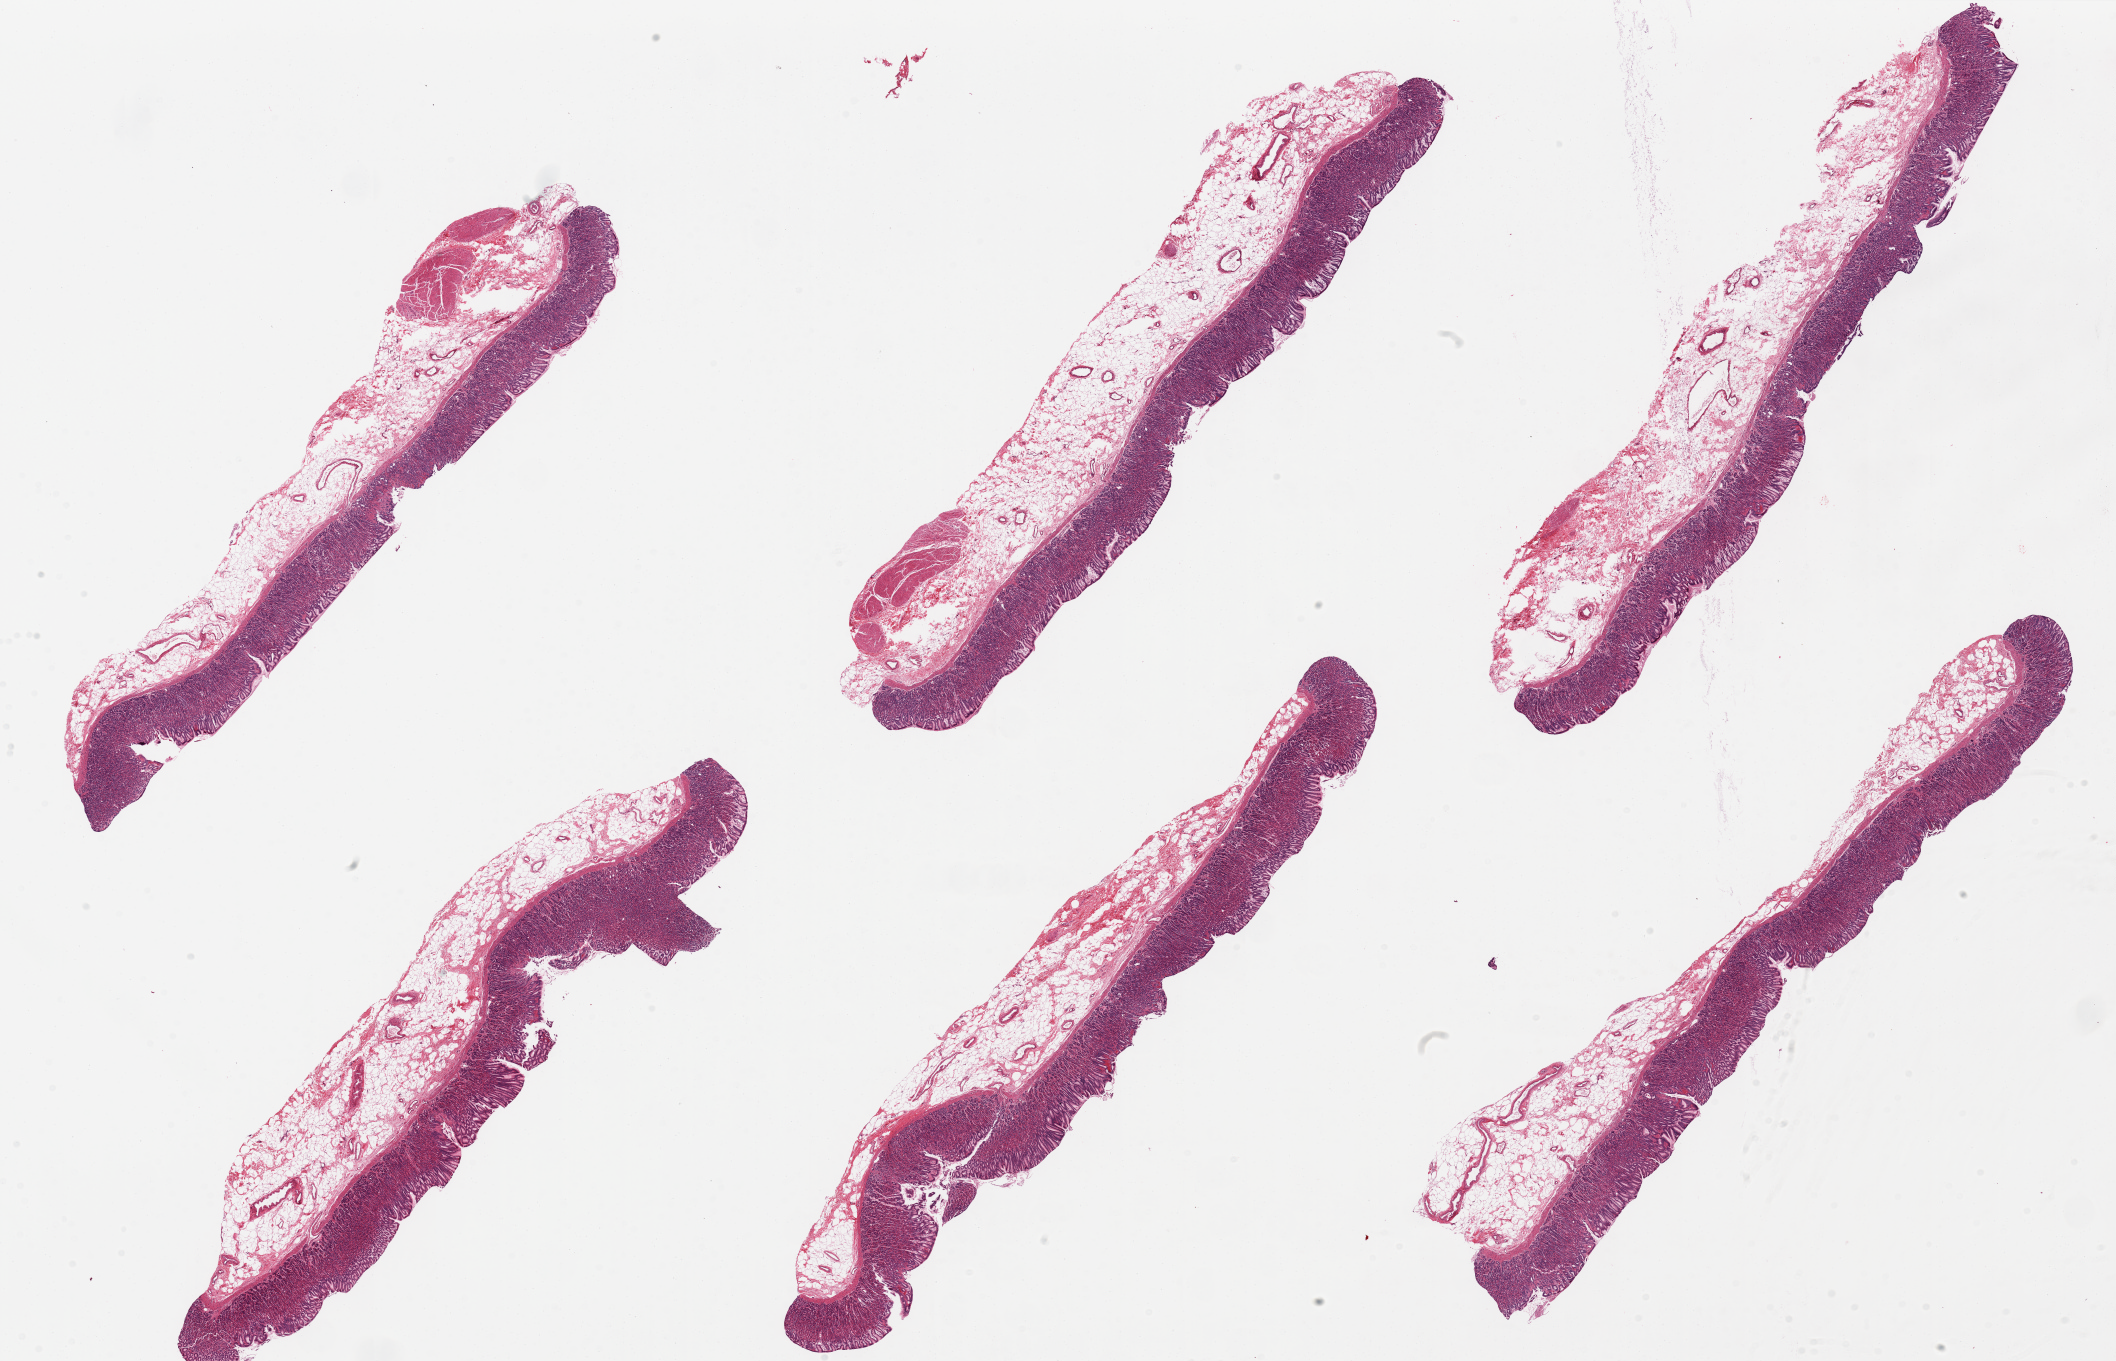
Haematoxylin and eosin whole-slide image, brightfield — shown as a low-resolution overview of the whole scanned area (about 33.5 x 21.5 mm); PAXgene-fixed paraffin-embedded (PFPE) section; section of stomach (target tissue); tissue donor sample. Donor sex: male.
Reviewer comment on this tissue sample: 6 pieces, few with small portion of muscularis.